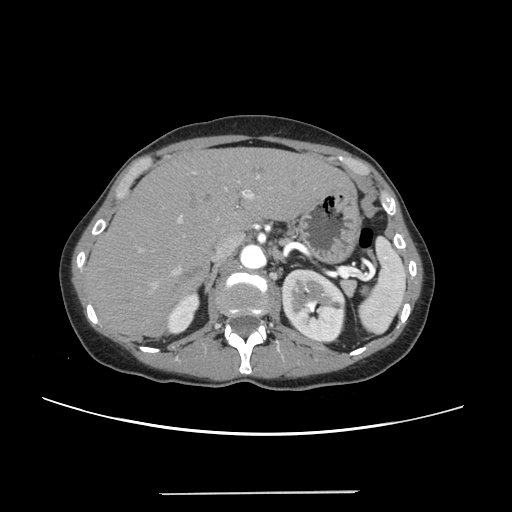
Contrast-enhanced abdominal CT, one axial slice; slice 164 of 240 in the series (ordered by position); intravenous contrast given; soft-tissue window (W 400 / L 40 HU); 1.25 mm slice thickness; 512 × 512 image matrix, field of view 371 × 371 mm. Female patient, age 60 years. Case-level facts recorded for this patient, not image findings: diagnosis: colorectal cancer liver metastases, imaged before liver resection; multiple liver metastases: no; largest metastasis: 1.5 cm; chemotherapy before resection: yes.
Outlined on this slice (manually delineated by an expert):
- liver: bounding box (x1, y1, x2, y2) in pixels: (87, 148, 348, 335)
- planned liver remnant (the part of the liver to remain after resection): (87, 148, 347, 335)
- portal vein (with intrahepatic branches): (139, 172, 259, 288)